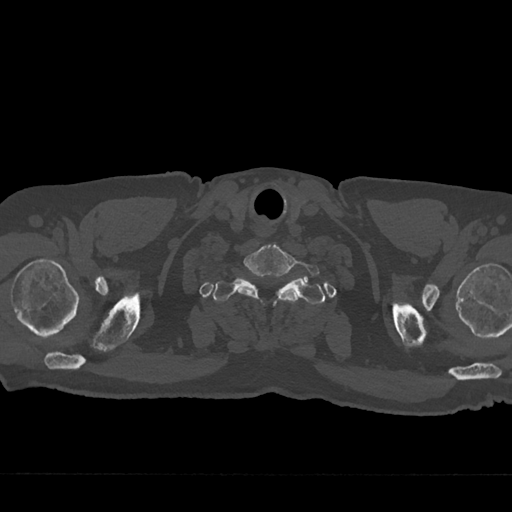
CT including the spine, one axial slice. Slice 677 of 797 in the series (ordered by position). Reconstruction kernel Br40s/3. Bone window (W 1800 / L 400 HU). 512 × 512 image matrix. Male patient, age 75 years. From the clinical record (not read from this slice): primary cancer: renal; vertebrae with lytic lesions (as recorded): T4.
Structures marked on this image (semi-automatic segmentation, software-assisted and operator-edited):
- T1 vertebra: bounding box [x1, y1, x2, y2] px = [213, 278, 324, 304]